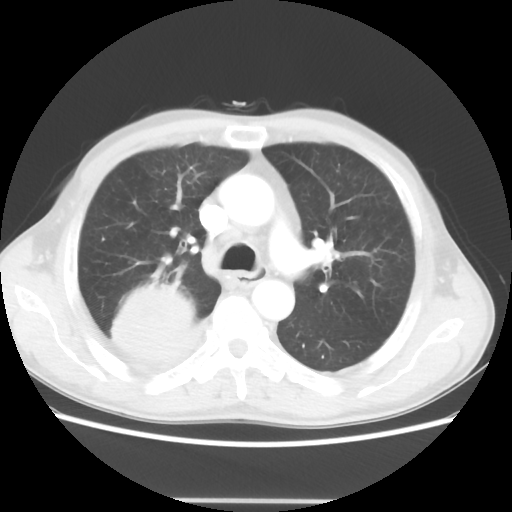
Chest CT, one axial slice; position 33 of 48 along the scan axis; reconstruction kernel STANDARD; lung window (W 1500 / L -600 HU); 5 mm slice thickness; 512 × 512 image matrix. Patient: male, 66 years. From the clinical record (not read from this slice): clinical TNM (as recorded): T4 N1 M1.
Annotated regions visible in this slice (rectangle marked by the reading radiologist):
- lung tumour (recorded histology: small cell carcinoma): box from (x=108, y=276) to (x=198, y=368) px